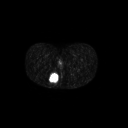
FDG PET of an extremity soft-tissue mass (from a PET/CT study), one axial slice. Slice 23 of 267 in the series (ordered by position). 128 × 128 image matrix. Patient: female, 17 years. From the clinical record (not read from this slice): histological type: epithelioid sarcoma; grade: intermediate; site of the primary tumour: right buttock.
Structures marked on this image (expert contour drawn on MRI and transferred to this co-registered scan by the dataset authors):
- gross tumour volume including surrounding oedema: bounding box (x1, y1, x2, y2) in pixels: (48, 72, 59, 84)
- gross tumour volume (mass): (49, 73, 59, 83)